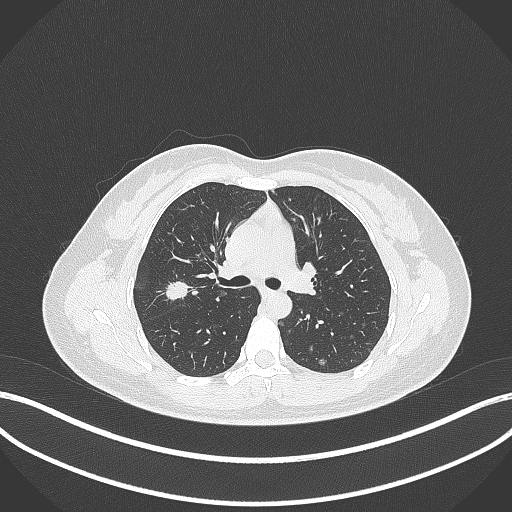
Chest CT, one axial slice. Position 214 of 307 along the scan axis. Reconstruction kernel B70f. Lung window (W 1500 / L -600 HU). 1 mm slice thickness. 512 × 512 image matrix, field of view 400 × 400 mm. Patient: female, 33 years. Case-level facts recorded for this patient, not image findings: clinical TNM (as recorded): T1c N0 M0; histopathological grade: G2-G3.
Annotated regions visible in this slice (rectangle marked by the reading radiologist):
- lung tumour (recorded histology: adenocarcinoma): bounding box [x1, y1, x2, y2] px = [162, 278, 191, 301]